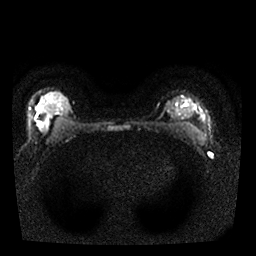
Breast MRI, one axial slice; position 16 of 25 along the scan axis; diffusion-weighted series; image 2 of 4 stored at this slice position (different b-values; order by instance number); 1.5 T; 256 × 256 image matrix, field of view 310 × 310 mm. Female patient.
Structures marked on this image (expert manual segmentation):
- tumour on diffusion-weighted imaging: bounding box [x1, y1, x2, y2] px = [44, 130, 47, 132]